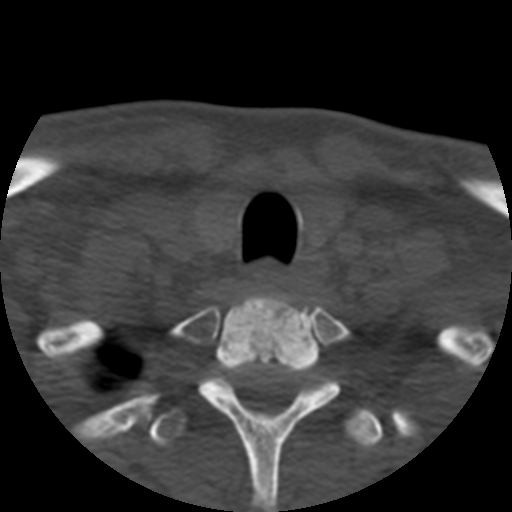
CT including the spine, one axial slice; position 445 of 508 along the scan axis; reconstruction kernel STANDARD; bone window (W 1800 / L 400 HU); 1.25 mm slice thickness; 512 × 512 image matrix, field of view 160 × 160 mm. Patient age 57 years. Case-level facts recorded for this patient, not image findings: primary cancer: prostate.
Annotated regions visible in this slice (semi-automatic segmentation, software-assisted and operator-edited):
- T1 vertebra: bounding box (x1, y1, x2, y2) in pixels: (167, 293, 385, 512)
- T2 vertebra: (146, 390, 387, 451)